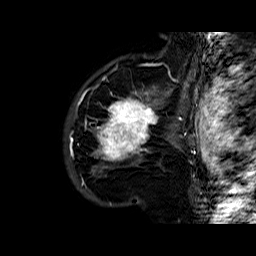
Breast MRI (dynamic contrast-enhanced), one sagittal slice; position 44 of 60 along the scan axis; dynamic contrast-enhanced series, time point 2 of 6 at this slice position (early post-contrast); 1.5 T; TE 6.4 ms, TR 32.8 ms; 4 mm slice thickness; 256 × 256 image matrix, field of view 200 × 200 mm. Female patient. From the clinical record (not read from this slice): setting: breast cancer imaged before/during neoadjuvant chemotherapy; receptor status: HR-positive, HER2-negative.
Annotated regions visible in this slice (semi-automatically segmented with operator editing):
- analysis volume of interest (the breast-tissue region the enhancement analysis was run in; not a lesion): box from (x=86, y=77) to (x=163, y=177) px
- tumour enhancement mask (voxels above the 100 % enhancement threshold inside the analysis volume of interest): (x=96, y=90)–(x=159, y=161)